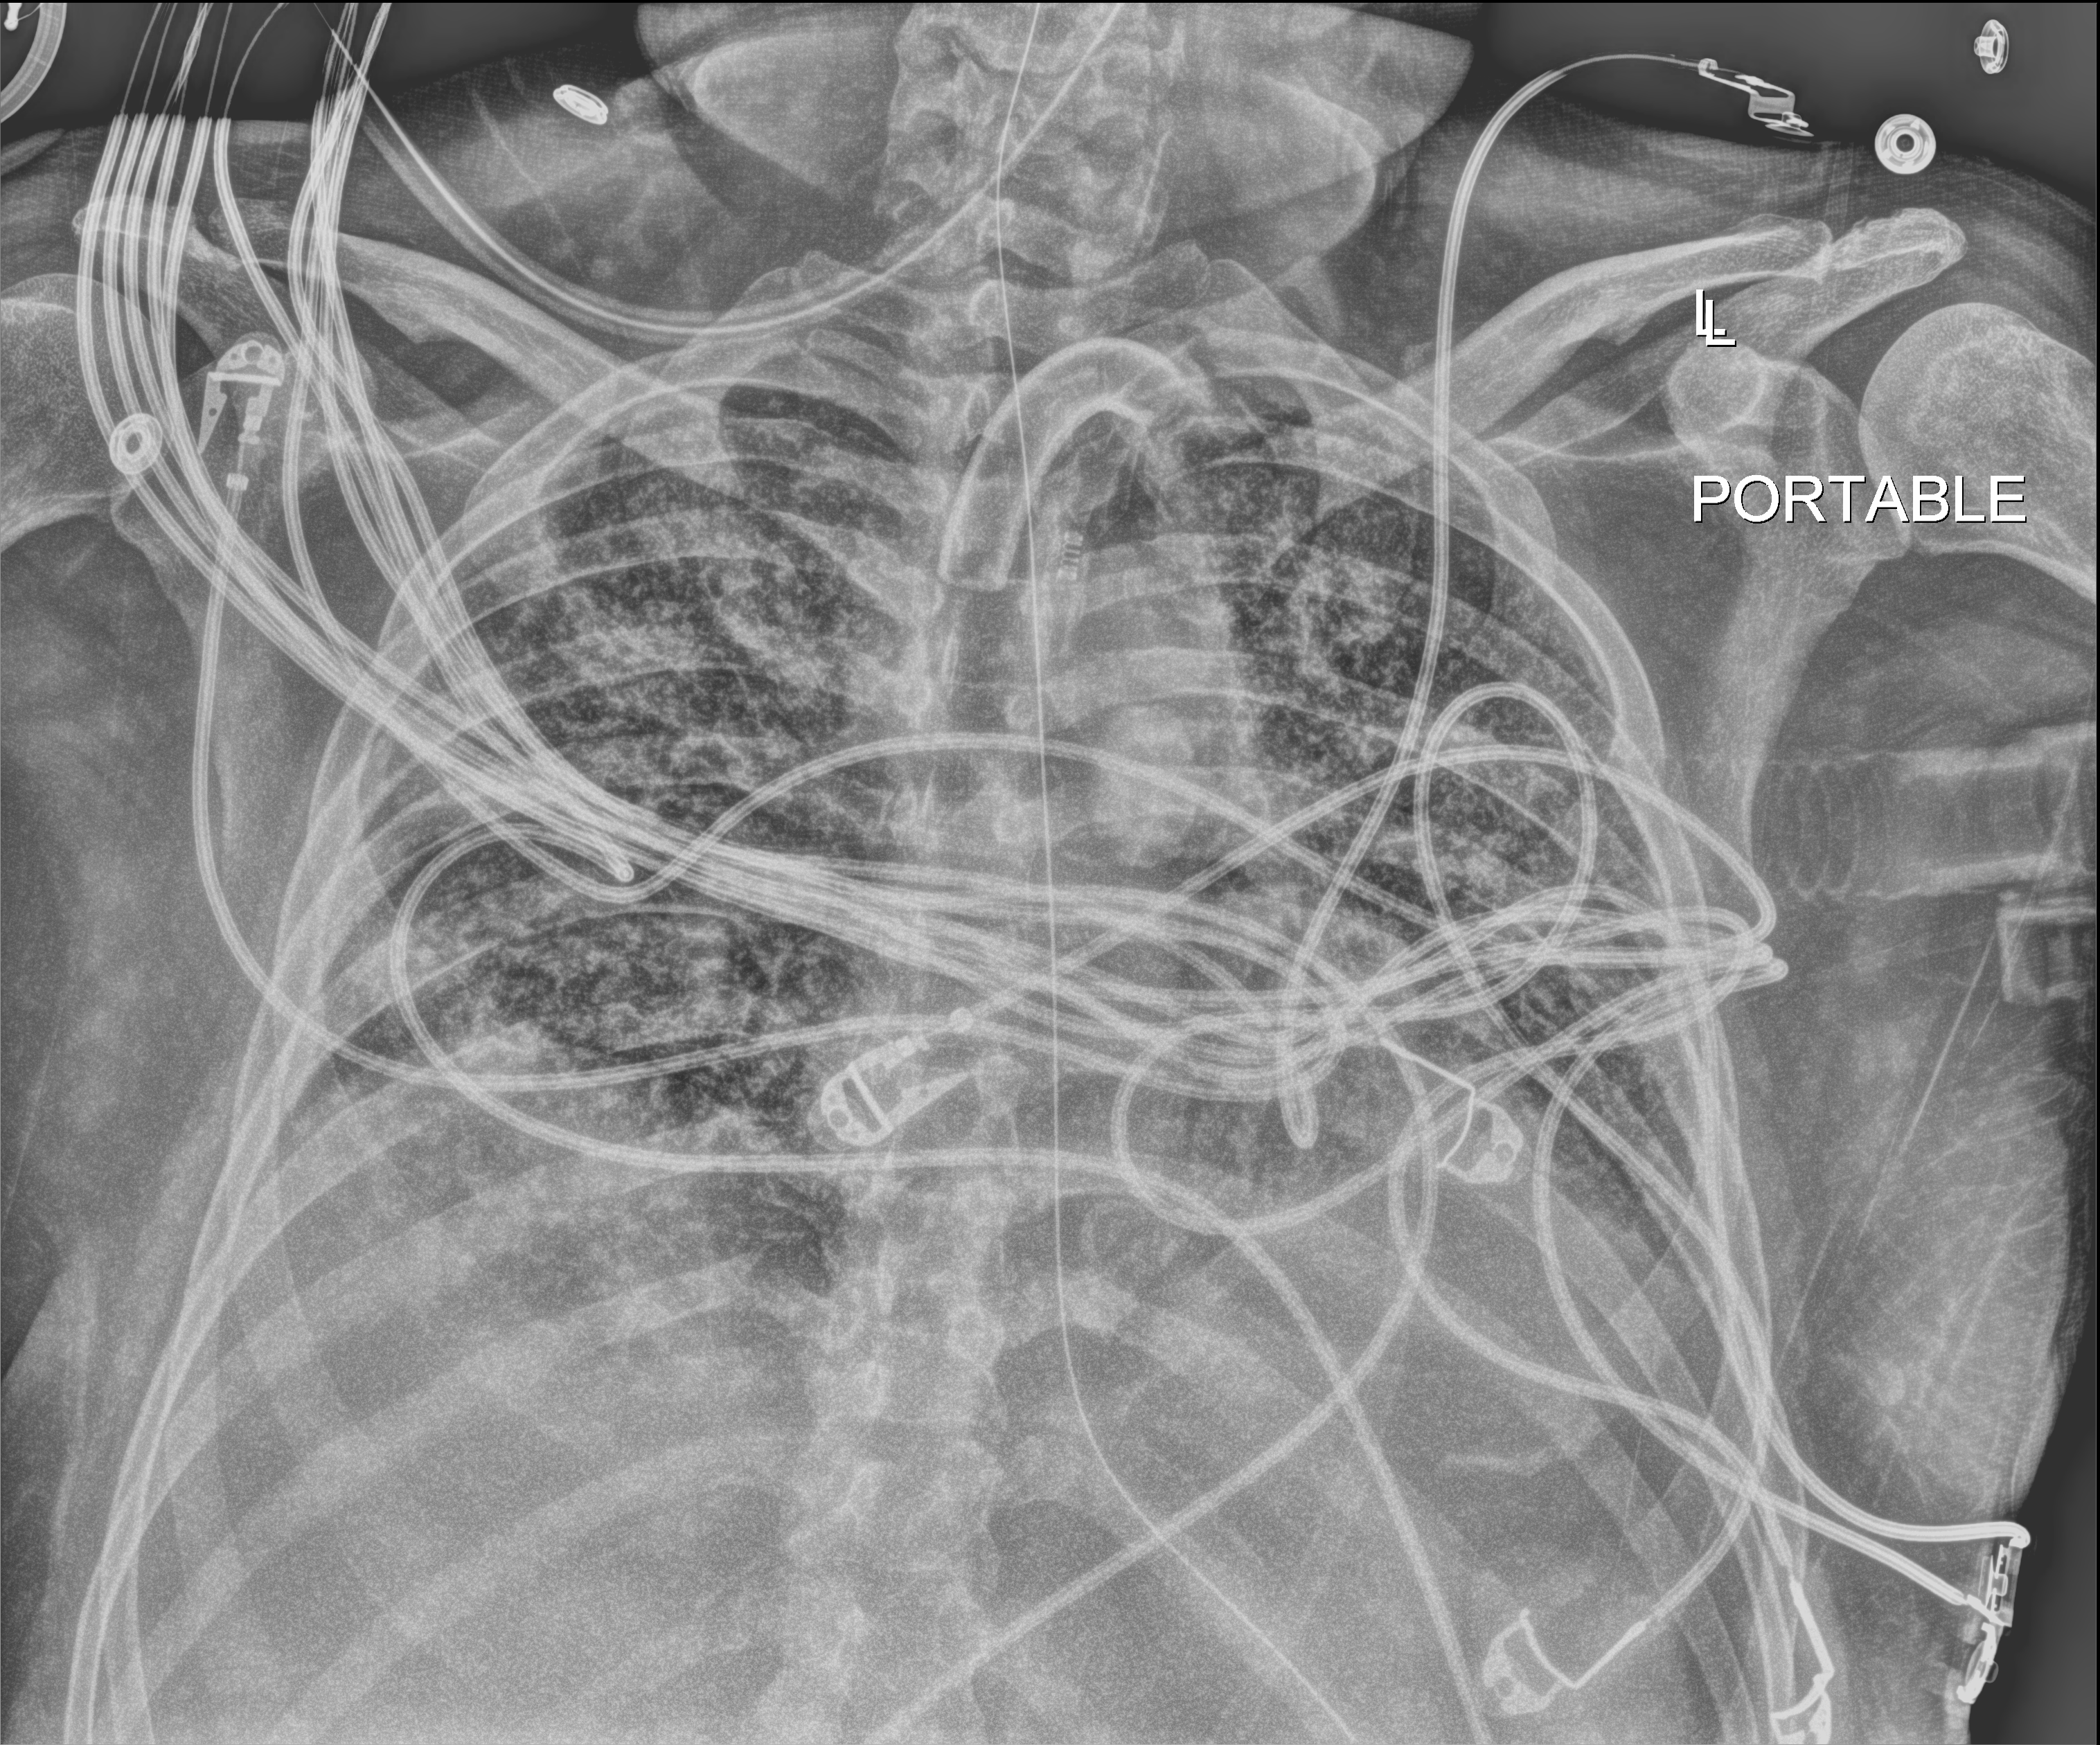
Chest X-ray (portable), anteroposterior (AP) projection. Male patient hospitalised with COVID-19, age 18–59 years.
From the hospital-stay record, not from the radiograph (when in the stay this image was taken is not recorded):
- mechanically ventilated during this hospital stay: yes